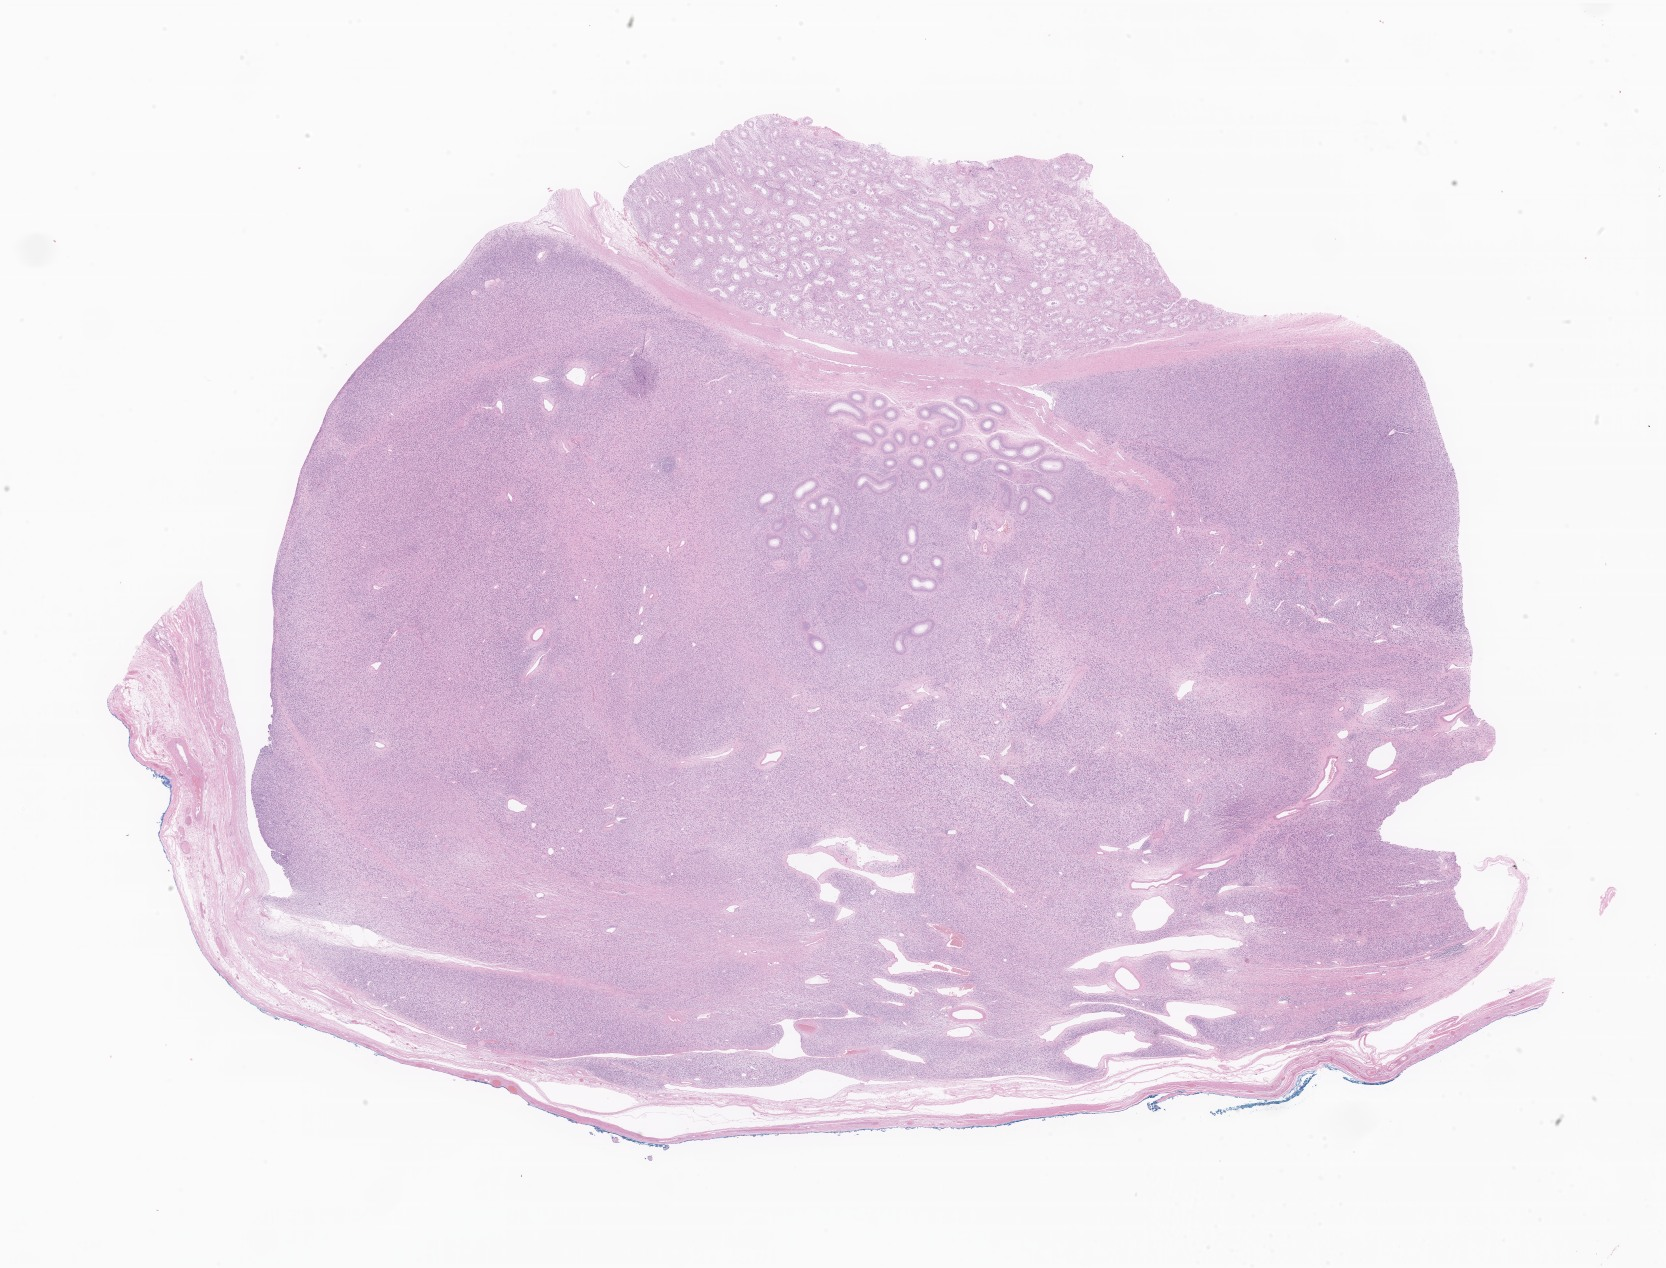
Digitized hematoxylin and eosin (H&E)-stained section of tumor tissue from the testis, low-resolution overview of the scanned area, about 28.1 x 21.4 mm. Formalin-fixed paraffin-embedded section. Male patient, age 178 months (14 years 10 months).
Diagnosis: Embryonal rhabdomyosarcoma, NOS.